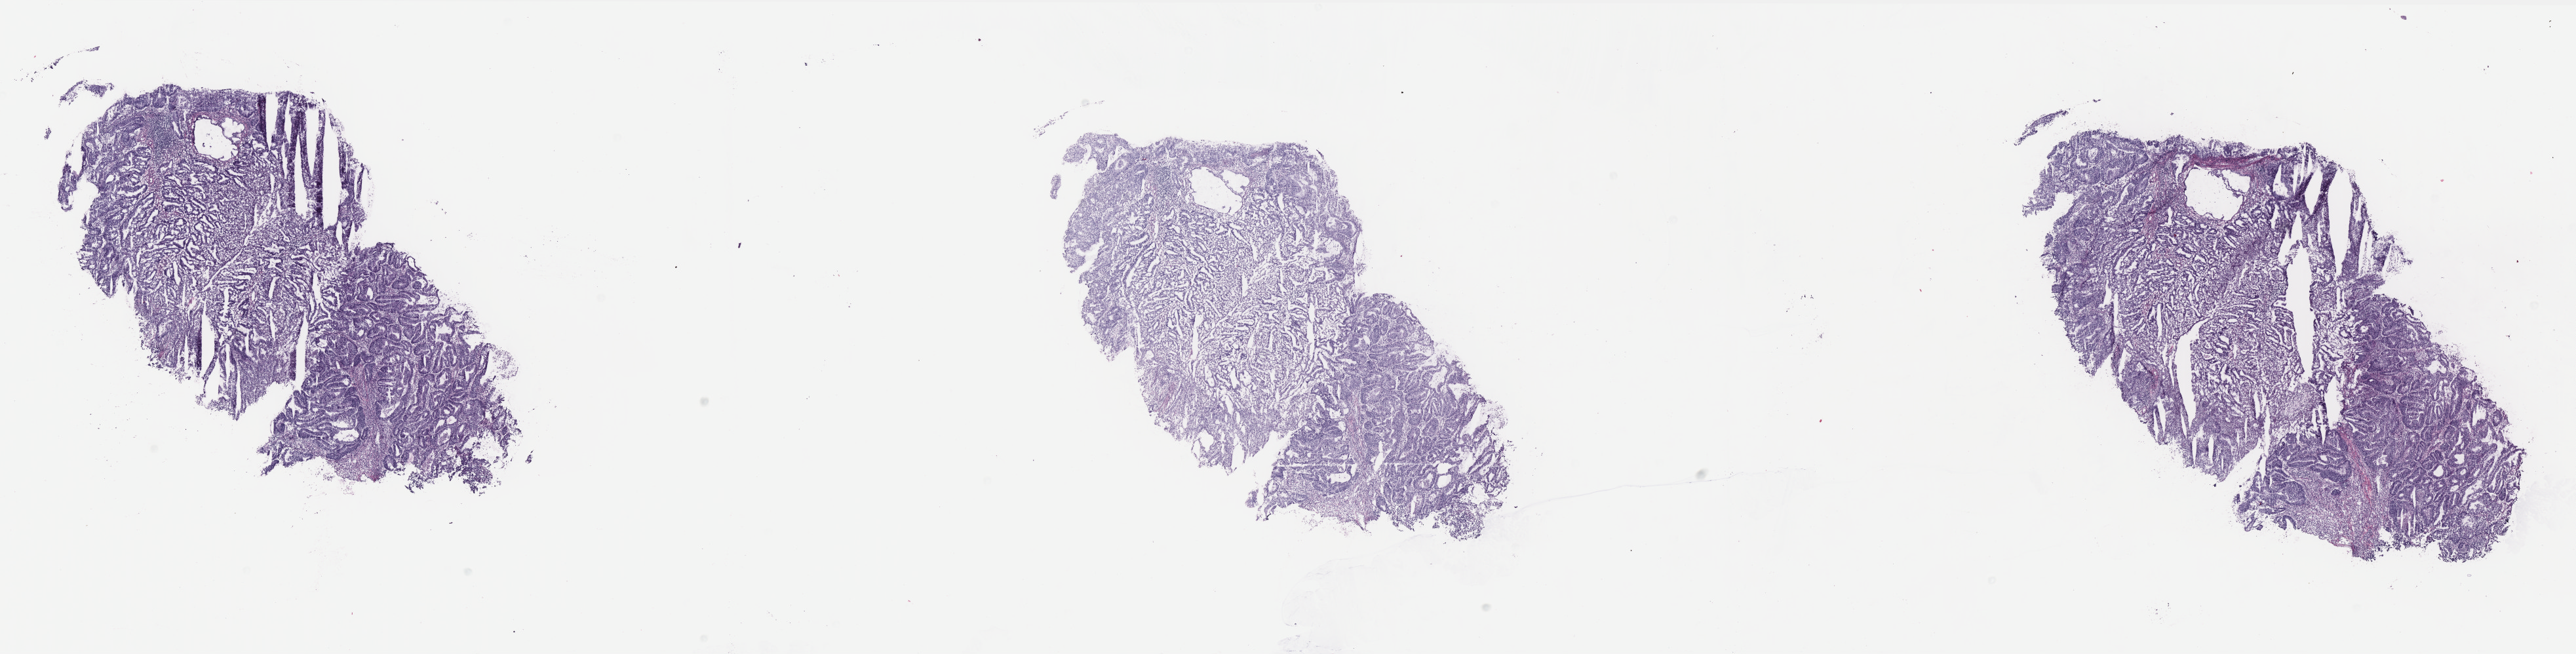
Whole-slide histology image, H&E-stained, shown as a low-resolution overview of the whole scanned area (about 31.5 x 8.0 mm, from a 40x scan). Frozen section. Sample: primary tumour, uterus. Female patient; age at initial diagnosis 76 years. Histologic grade: G1 (well differentiated). Slide review estimates, as recorded: tumour cells 70%, tumour nuclei 70%, normal cells 0%, stromal cells 25%, necrosis 5%. Infiltration values recorded for this section: lymphocyte infiltration 35%, monocyte infiltration 20%, neutrophil infiltration 25%.
FIGO stage: IB. Pathologic diagnosis: Endometrioid adenocarcinoma, NOS (endometrium).